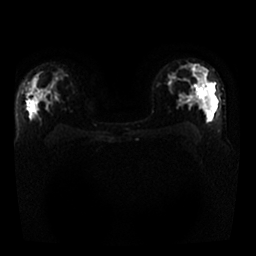
Breast MRI, one axial slice. Position 17 of 25 along the scan axis. Diffusion-weighted series; image 2 of 4 stored at this slice position (different b-values; order by instance number). 1.5 T. 256 × 256 image matrix. Female patient.
Outlined on this slice (manually delineated by an expert):
- tumour on diffusion-weighted imaging: bounding box (x1, y1, x2, y2) in pixels: (29, 88, 34, 95)